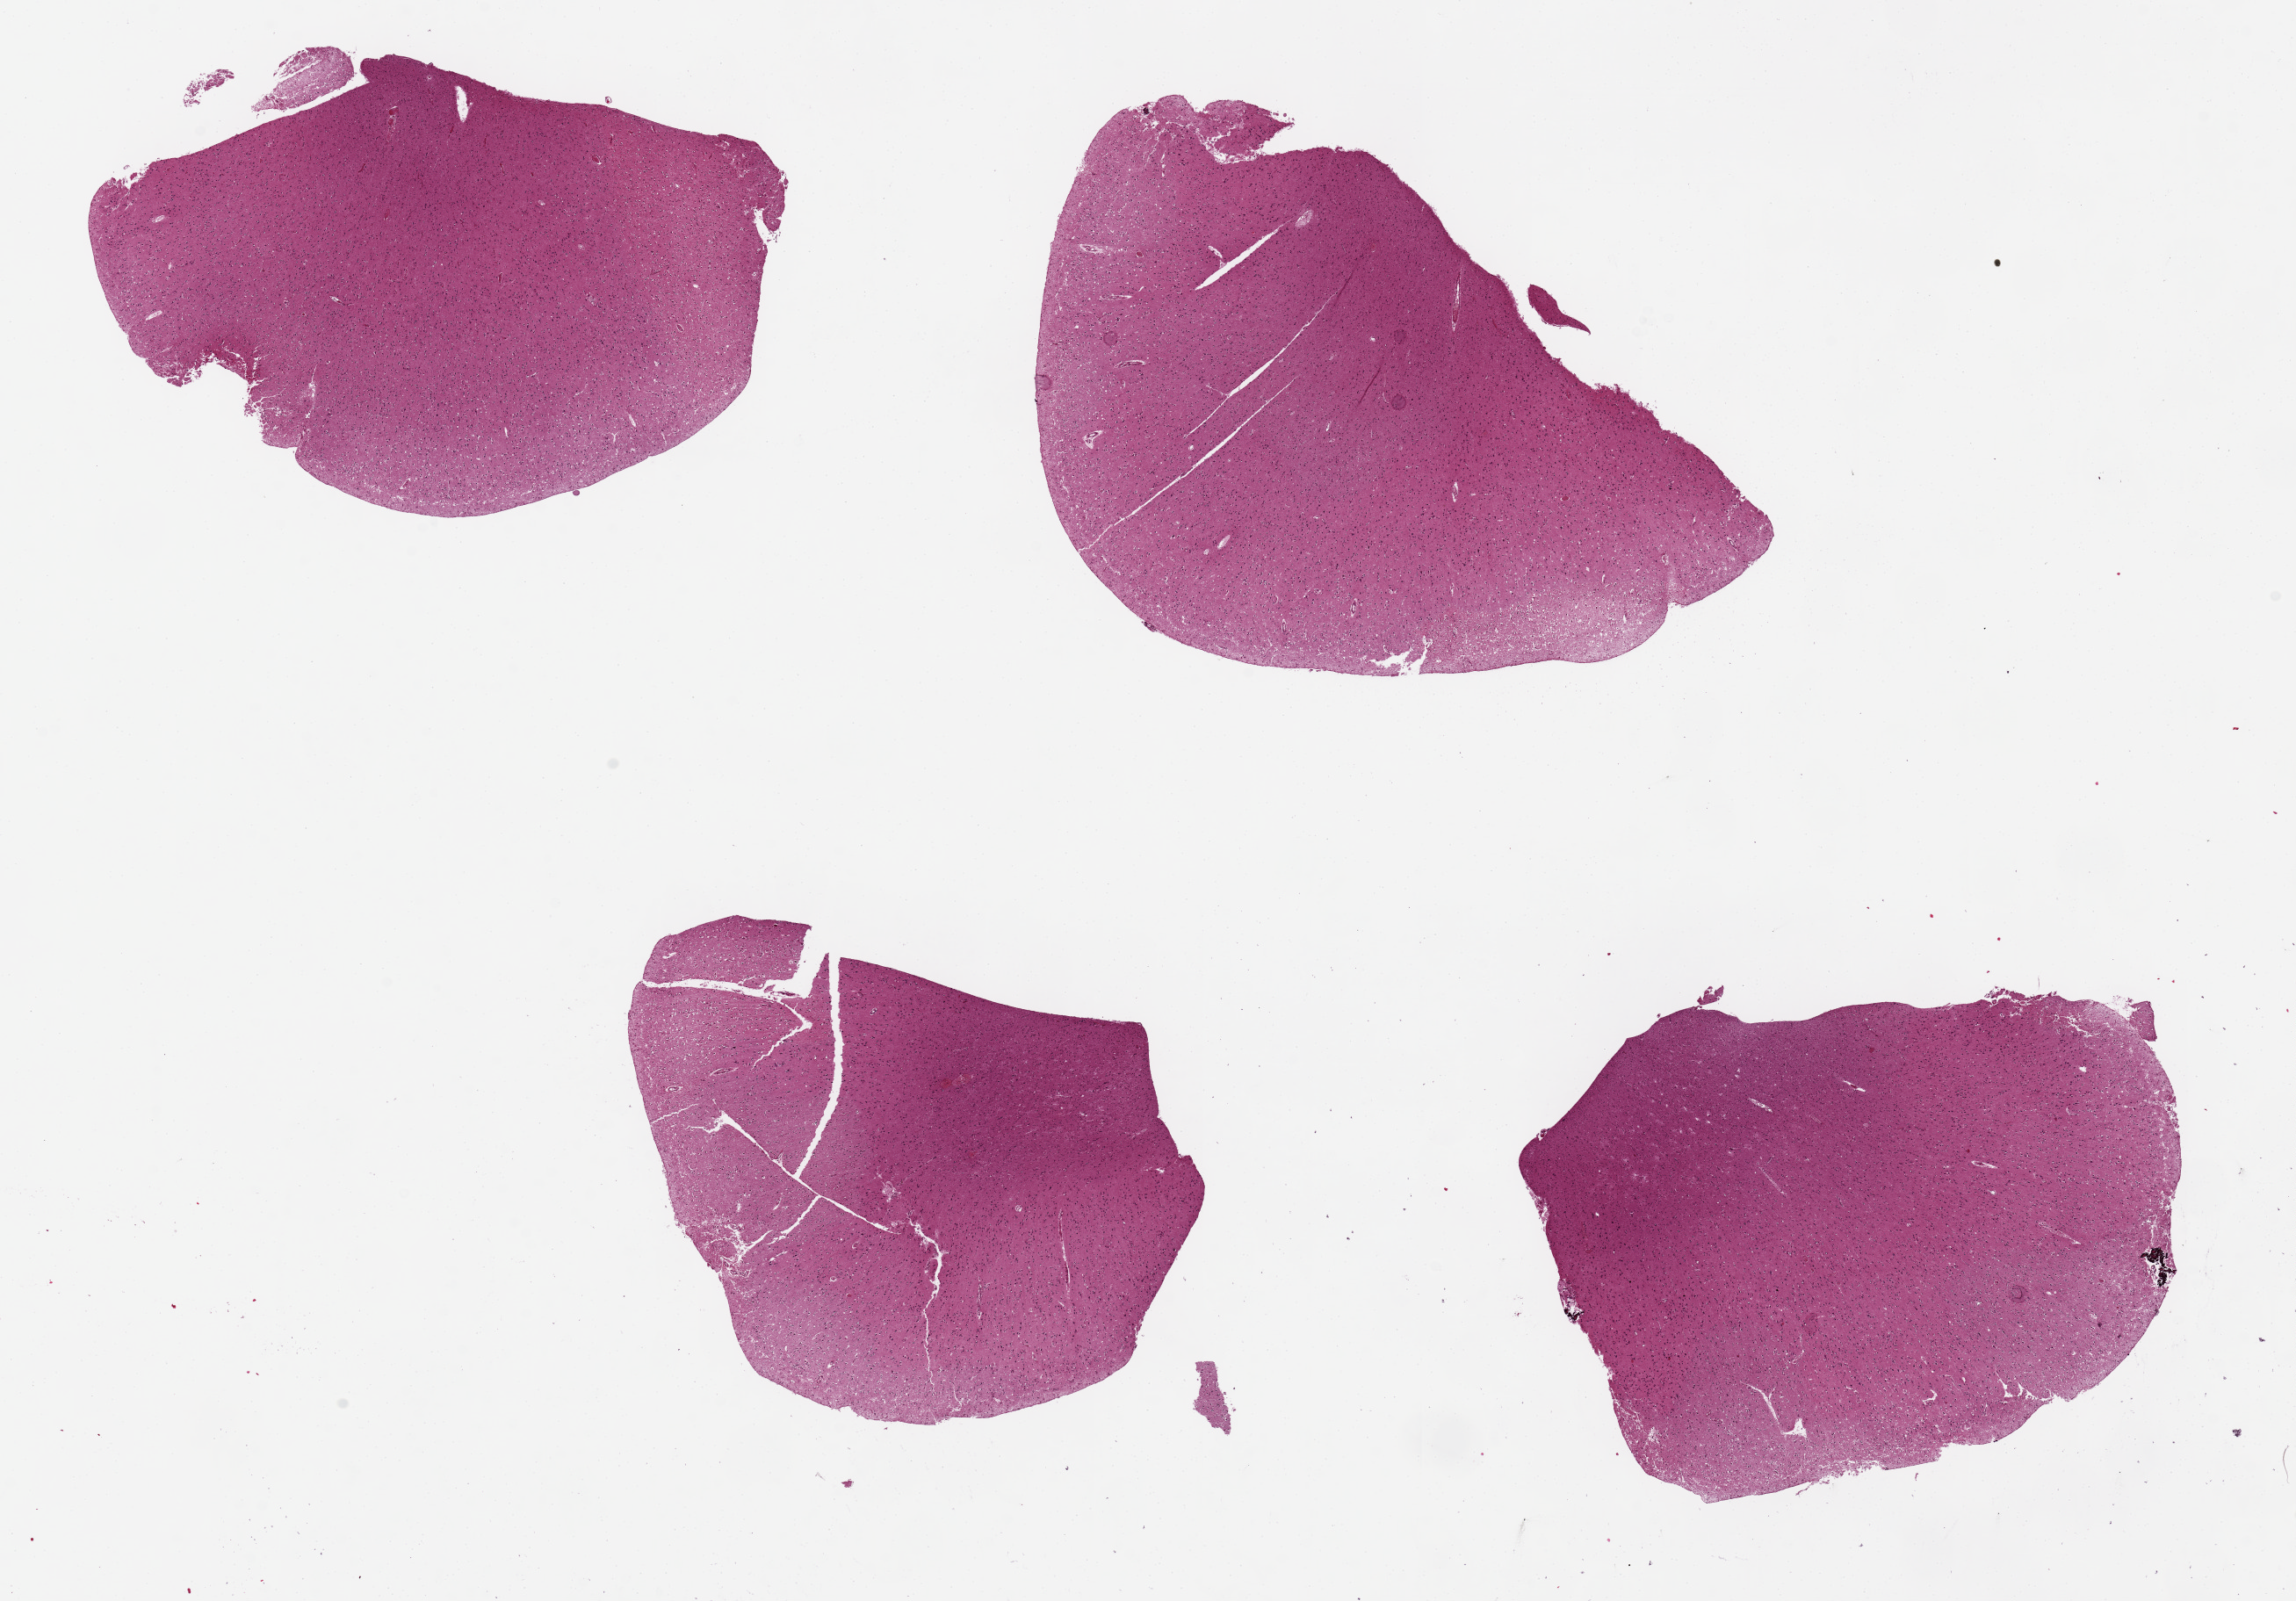
Whole-slide image, haematoxylin and eosin stain — low-resolution overview of the scanned area, about 20.7 x 14.4 mm, PAXgene-fixed paraffin-embedded (PFPE) section, section of cerebral cortex (target tissue), tissue donor sample. Donor sex: female.
* reviewer comment on this tissue sample: 4 pieces, ~6x4mm